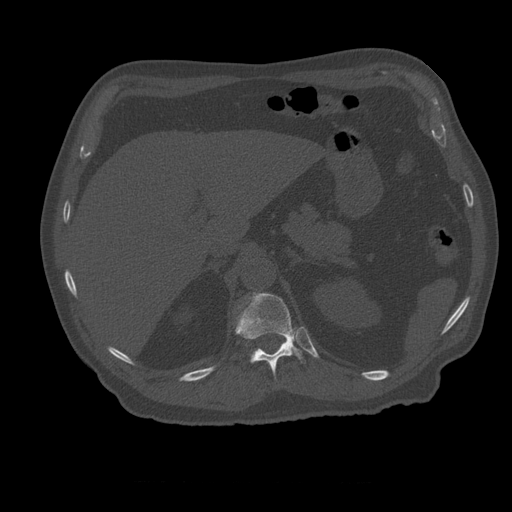
CT including the spine, one axial slice; position 259 of 399 along the scan axis; 120 kVp; bone window (W 1800 / L 400 HU); 512 × 512 image matrix. Patient age 73 years. From the clinical record (not read from this slice): primary cancer: prostate; vertebrae with lytic lesions (as recorded): L2.
Outlined on this slice (semi-automatic segmentation, software-assisted and operator-edited):
- T12 vertebra: bounding box [x1, y1, x2, y2] px = [235, 293, 303, 375]